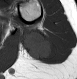
MRI of an extremity soft-tissue mass, one axial slice. Slice 13 of 28 in the series (ordered by position). MR volume resampled by the dataset authors to the PET/CT grid (not the native acquisition matrix). 3.27 mm slice thickness. 77 × 79 image matrix, field of view 75 × 77 mm. Female patient. Case-level facts recorded for this patient, not image findings: histological type: malignant fibrous histiocytoma; grade: low; site of the primary tumour: left arm.
Outlined on this slice (expert contour drawn on MRI and transferred to this co-registered scan by the dataset authors):
- gross tumour volume (mass): bounding box (x1, y1, x2, y2) in pixels: (19, 27, 57, 62)